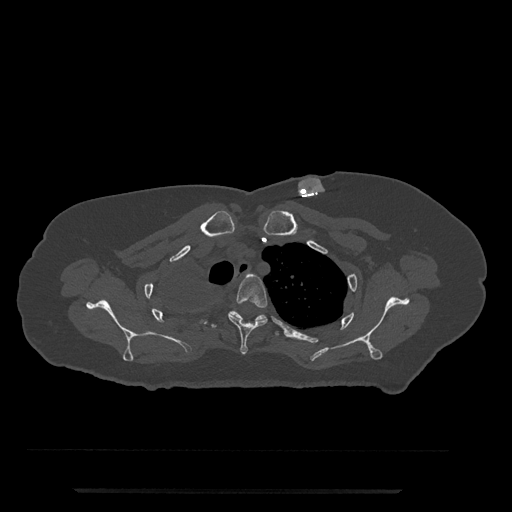
CT including the spine, one axial slice. Position 622 of 797 along the scan axis. Reconstruction kernel Br40s/3. Bone window (W 1800 / L 400 HU). 512 × 512 image matrix, field of view 440 × 440 mm. Patient: female, 51 years. From the clinical record (not read from this slice): primary cancer: neuro.
Annotated regions visible in this slice (semi-automatically segmented with operator editing):
- T3 vertebra: bounding box (x1, y1, x2, y2) in pixels: (228, 274, 268, 355)
- T4 vertebra: (211, 310, 279, 336)